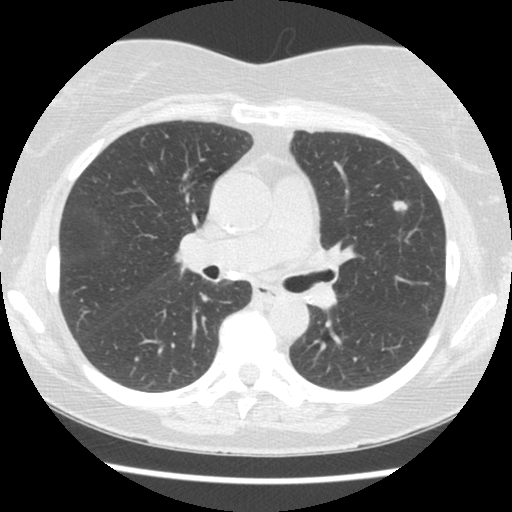
Low-dose screening chest CT, one axial slice. Slice 69 of 120 in the series (ordered by position). Reconstruction kernel STANDARD. Lung window (W 1500 / L -600 HU). 2.5 mm slice thickness. 512 × 512 image matrix, field of view 310 × 310 mm.
Annotated regions visible in this slice (outlined manually by an expert reader):
- lesion 1 (tumor, upper lobe of left lung): bounding box (x1, y1, x2, y2) in pixels: (393, 201, 408, 211)